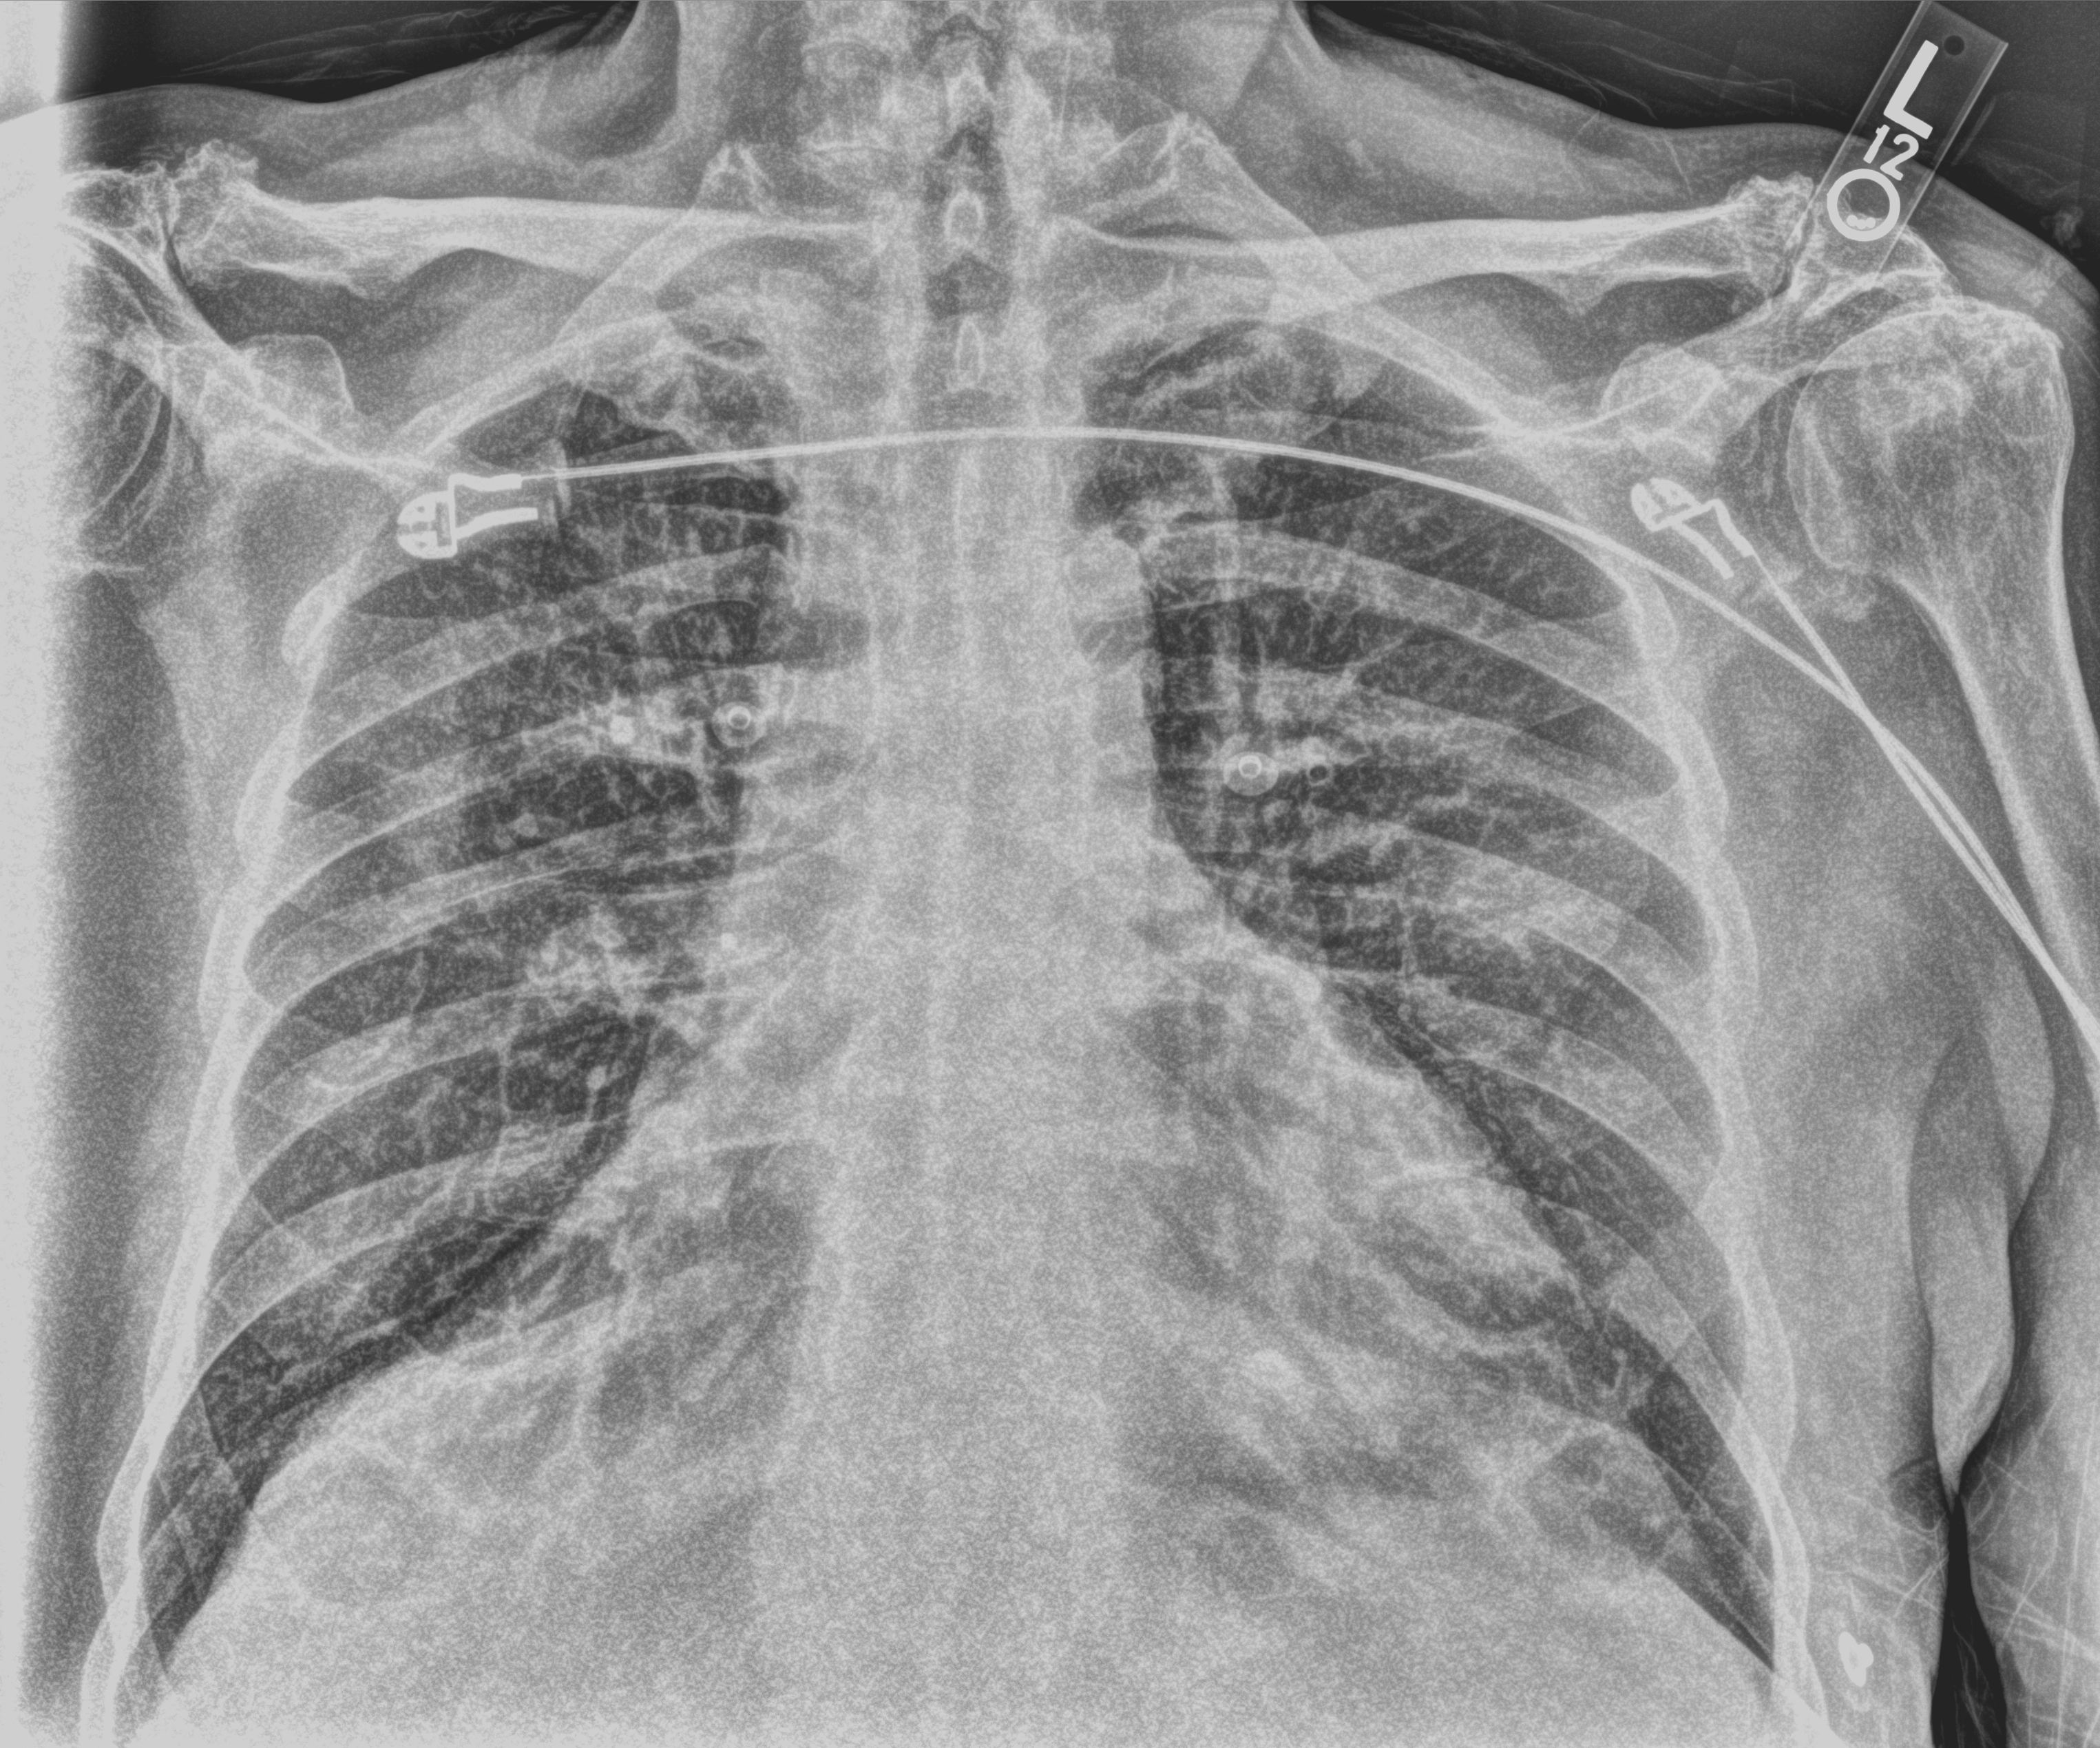
Bedside chest radiograph (computed radiography). Male patient hospitalised with COVID-19, age 75–90 years.
Hospital-stay facts (about this admission, not read from this image; timing relative to this image not recorded):
- admitted to intensive care during this hospital stay: no